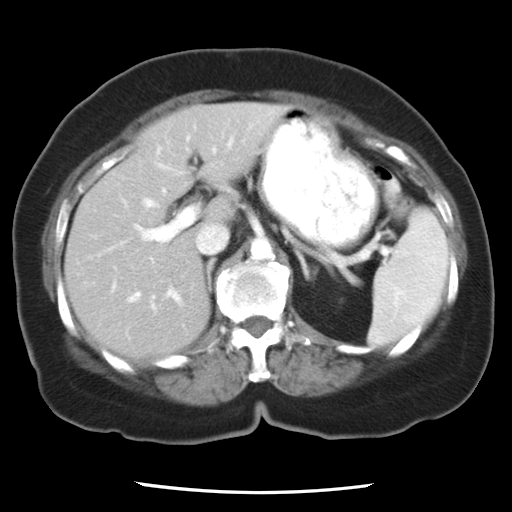
Contrast-enhanced abdominal CT, one axial slice; position 14 of 24 along the scan axis; reconstruction kernel STANDARD; 120 kVp; intravenous contrast given; soft-tissue window (W 400 / L 40 HU); 7.5 mm slice thickness; 512 × 512 image matrix, field of view 312 × 312 mm. Female patient, age 71 years. Case-level facts recorded for this patient, not image findings: diagnosis: colorectal cancer liver metastases, imaged before liver resection.
Outlined on this slice (expert manual segmentation):
- hepatic veins: bounding box (x1, y1, x2, y2) in pixels: (129, 189, 200, 365)
- liver: (66, 103, 285, 360)
- planned liver remnant (the part of the liver to remain after resection): (66, 115, 232, 360)
- portal vein (with intrahepatic branches): (104, 149, 216, 305)